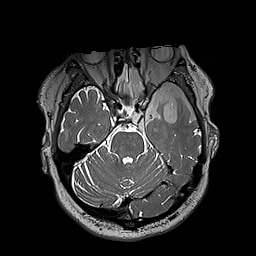
Brain MRI from a brain-tumour surgery series, one axial slice; slice 139 of 192 in the series (ordered by position); 1 mm slice thickness; 256 × 256 image matrix. From the clinical record (not read from this slice): histopathology: Oligodendroglioma; WHO grade: 3; IDH mutation: yes; tumour location: Left Sylvian Fissure (Temporal).
Outlined on this slice (manually delineated by an expert):
- tumour: bounding box [x1, y1, x2, y2] px = [124, 66, 197, 122]